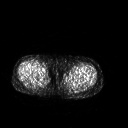
FDG PET of an extremity soft-tissue mass (from a PET/CT study), one axial slice; slice 221 of 267 in the series (ordered by position); 3.27 mm slice thickness; 128 × 128 image matrix, field of view 500 × 500 mm. Patient: female, 42 years. Case-level facts recorded for this patient, not image findings: histological type: pleiomorphic leiomyosarcoma; grade: intermediate; site of the primary tumour: left thigh.
Structures marked on this image (expert contour drawn on MRI and transferred to this co-registered scan by the dataset authors):
- gross tumour volume including surrounding oedema: box from (x=66, y=73) to (x=81, y=80) px